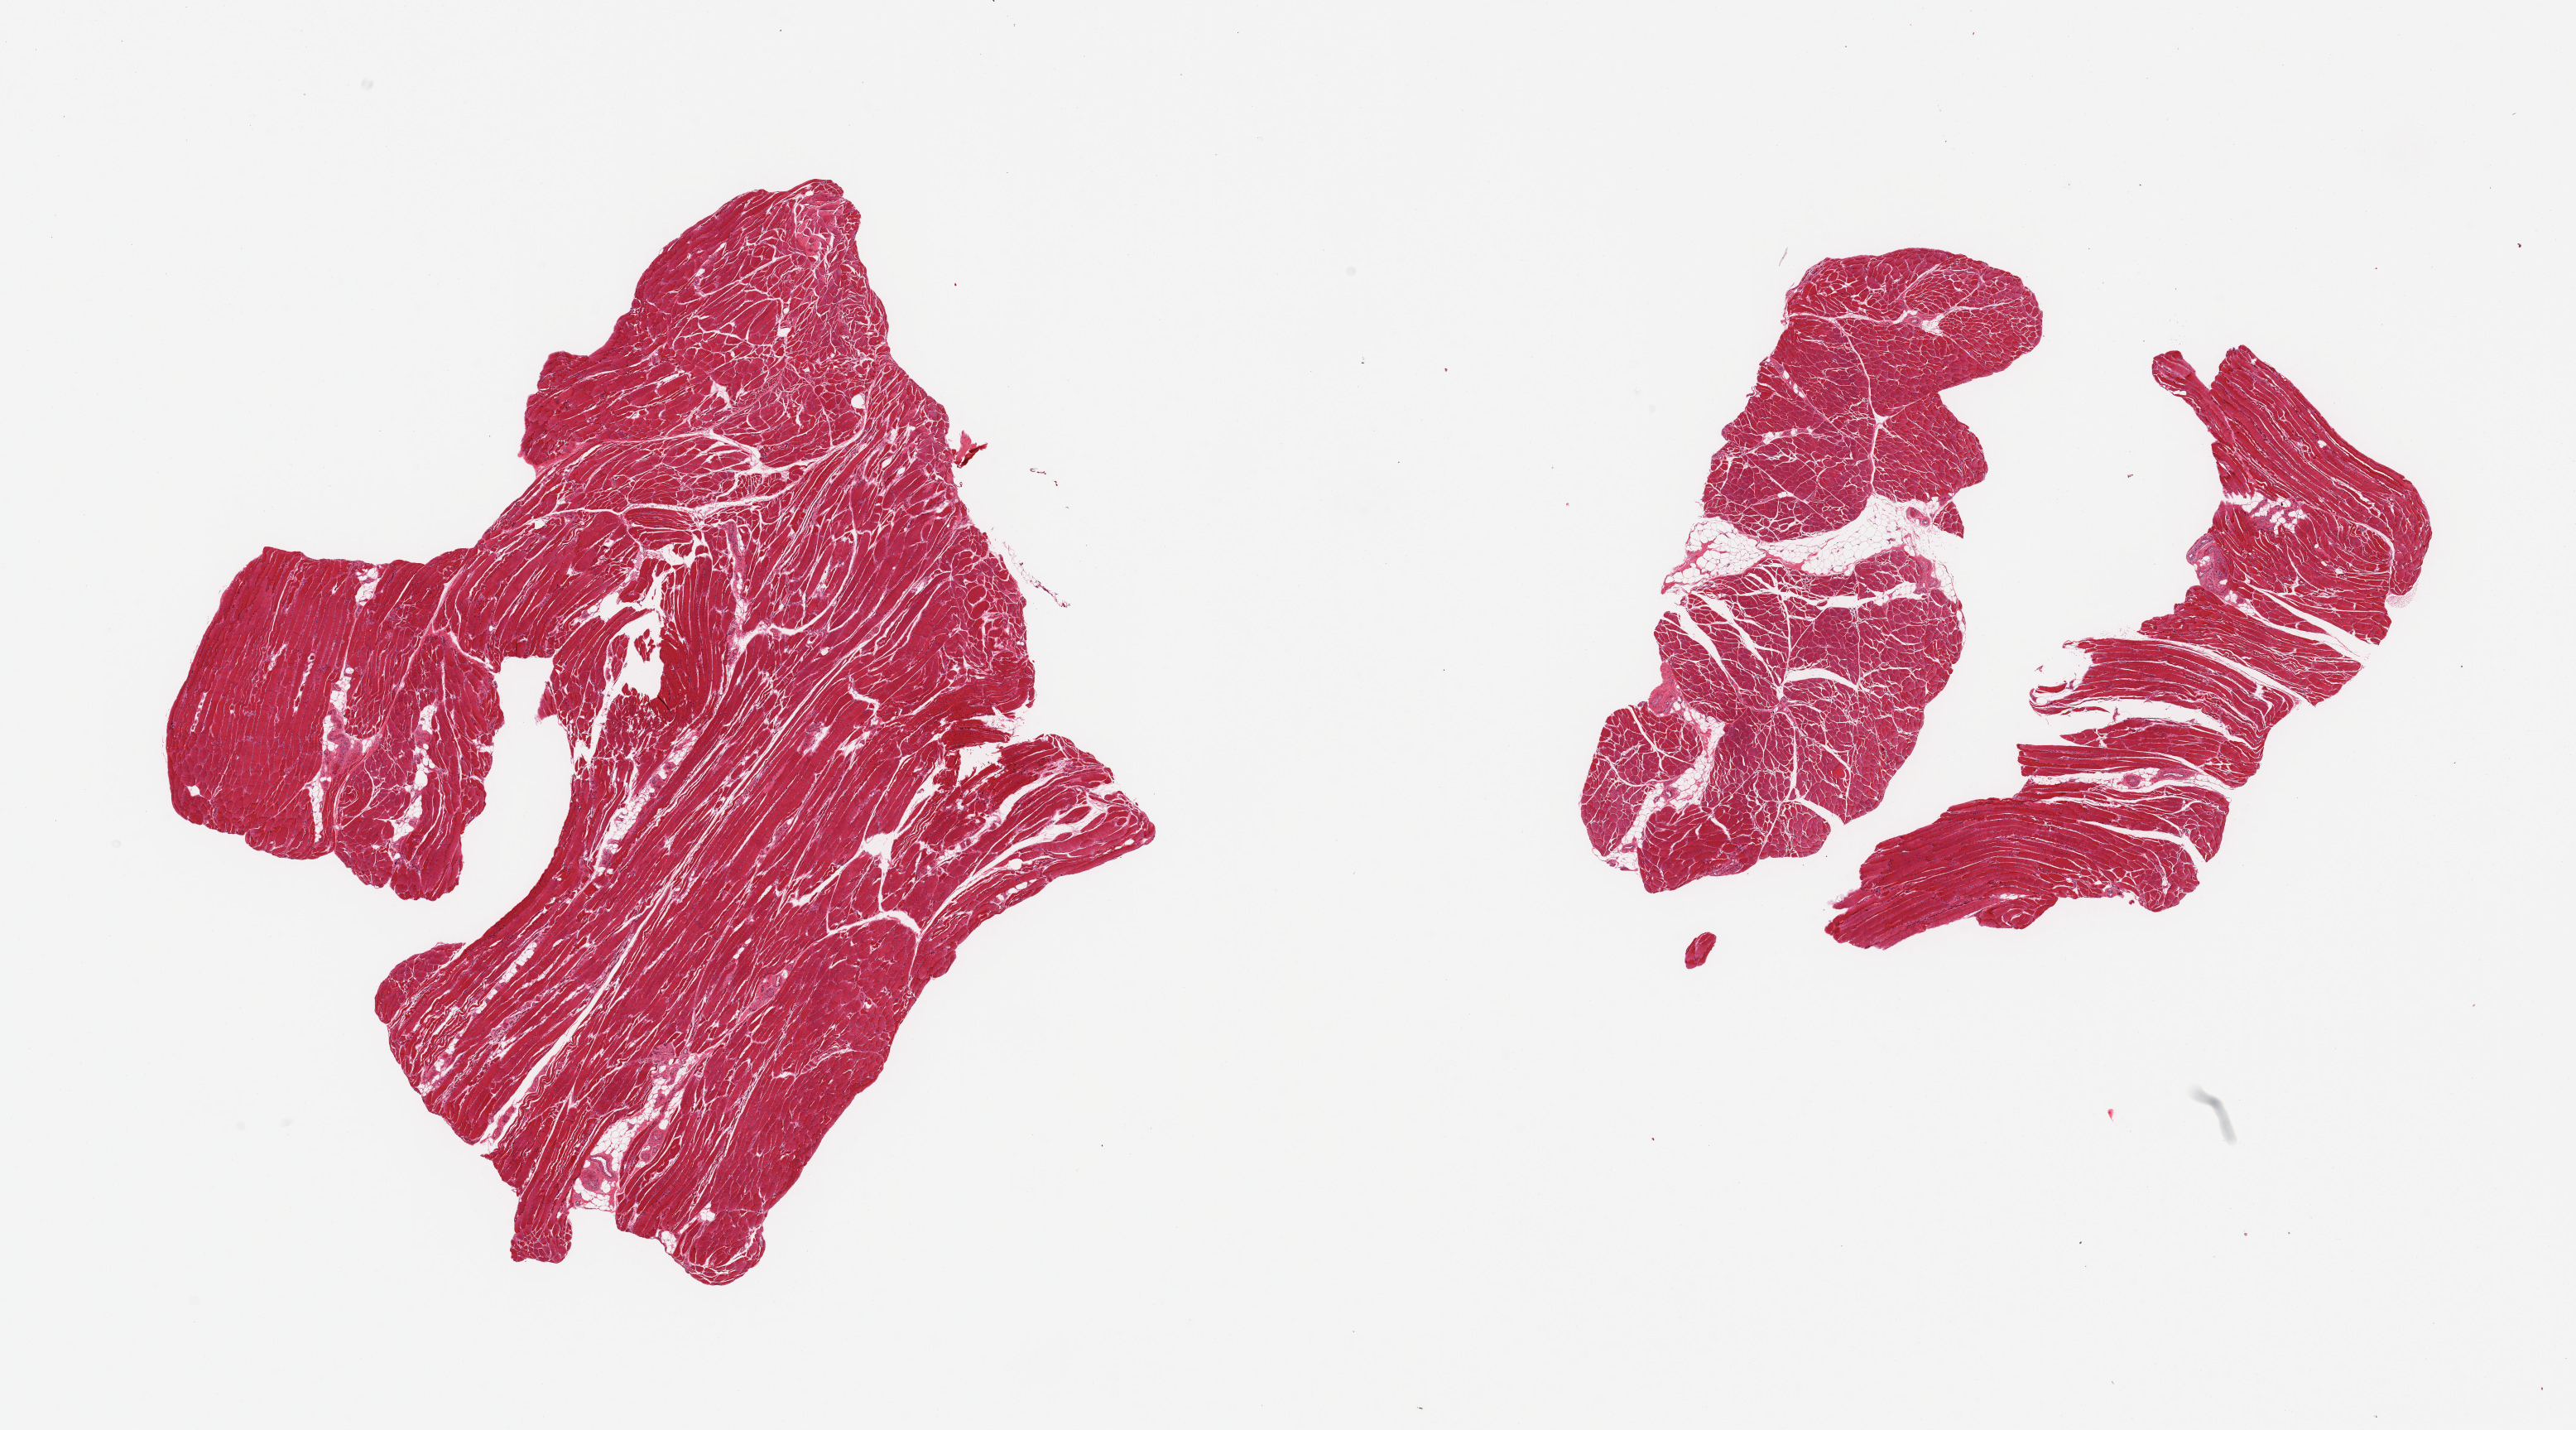
Whole-slide image, hematoxylin and eosin (H&E) stain — shown as a low-resolution overview of the whole scanned area (about 24.6 x 13.7 mm). PAXgene-fixed paraffin-embedded (PFPE) section. Sampled site (target tissue): skeletal muscle. Donor tissue sample.
Pathologist's review note for this sample: 2 pieces; small amounts of internal fat, scattered atrophic fibers.